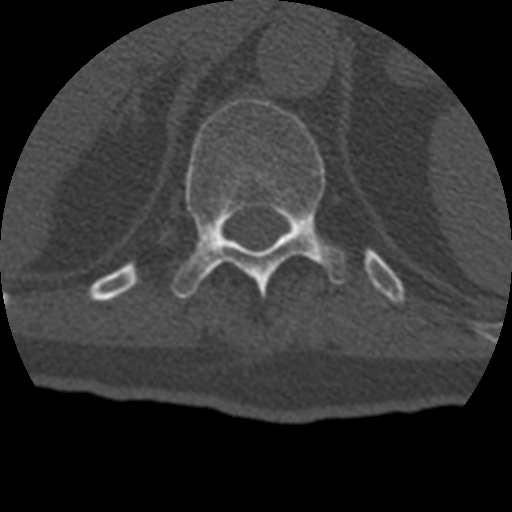
CT including the spine, one axial slice. Position 197 of 399 along the scan axis. Reconstruction kernel STANDARD. Bone window (W 1800 / L 400 HU). 1.25 mm slice thickness. 512 × 512 image matrix, field of view 160 × 160 mm. Patient age 69 years. From the clinical record (not read from this slice): primary cancer: prostate.
Structures marked on this image (semi-automatically segmented with operator editing):
- T11 vertebra: box from (x=172, y=97) to (x=348, y=299) px